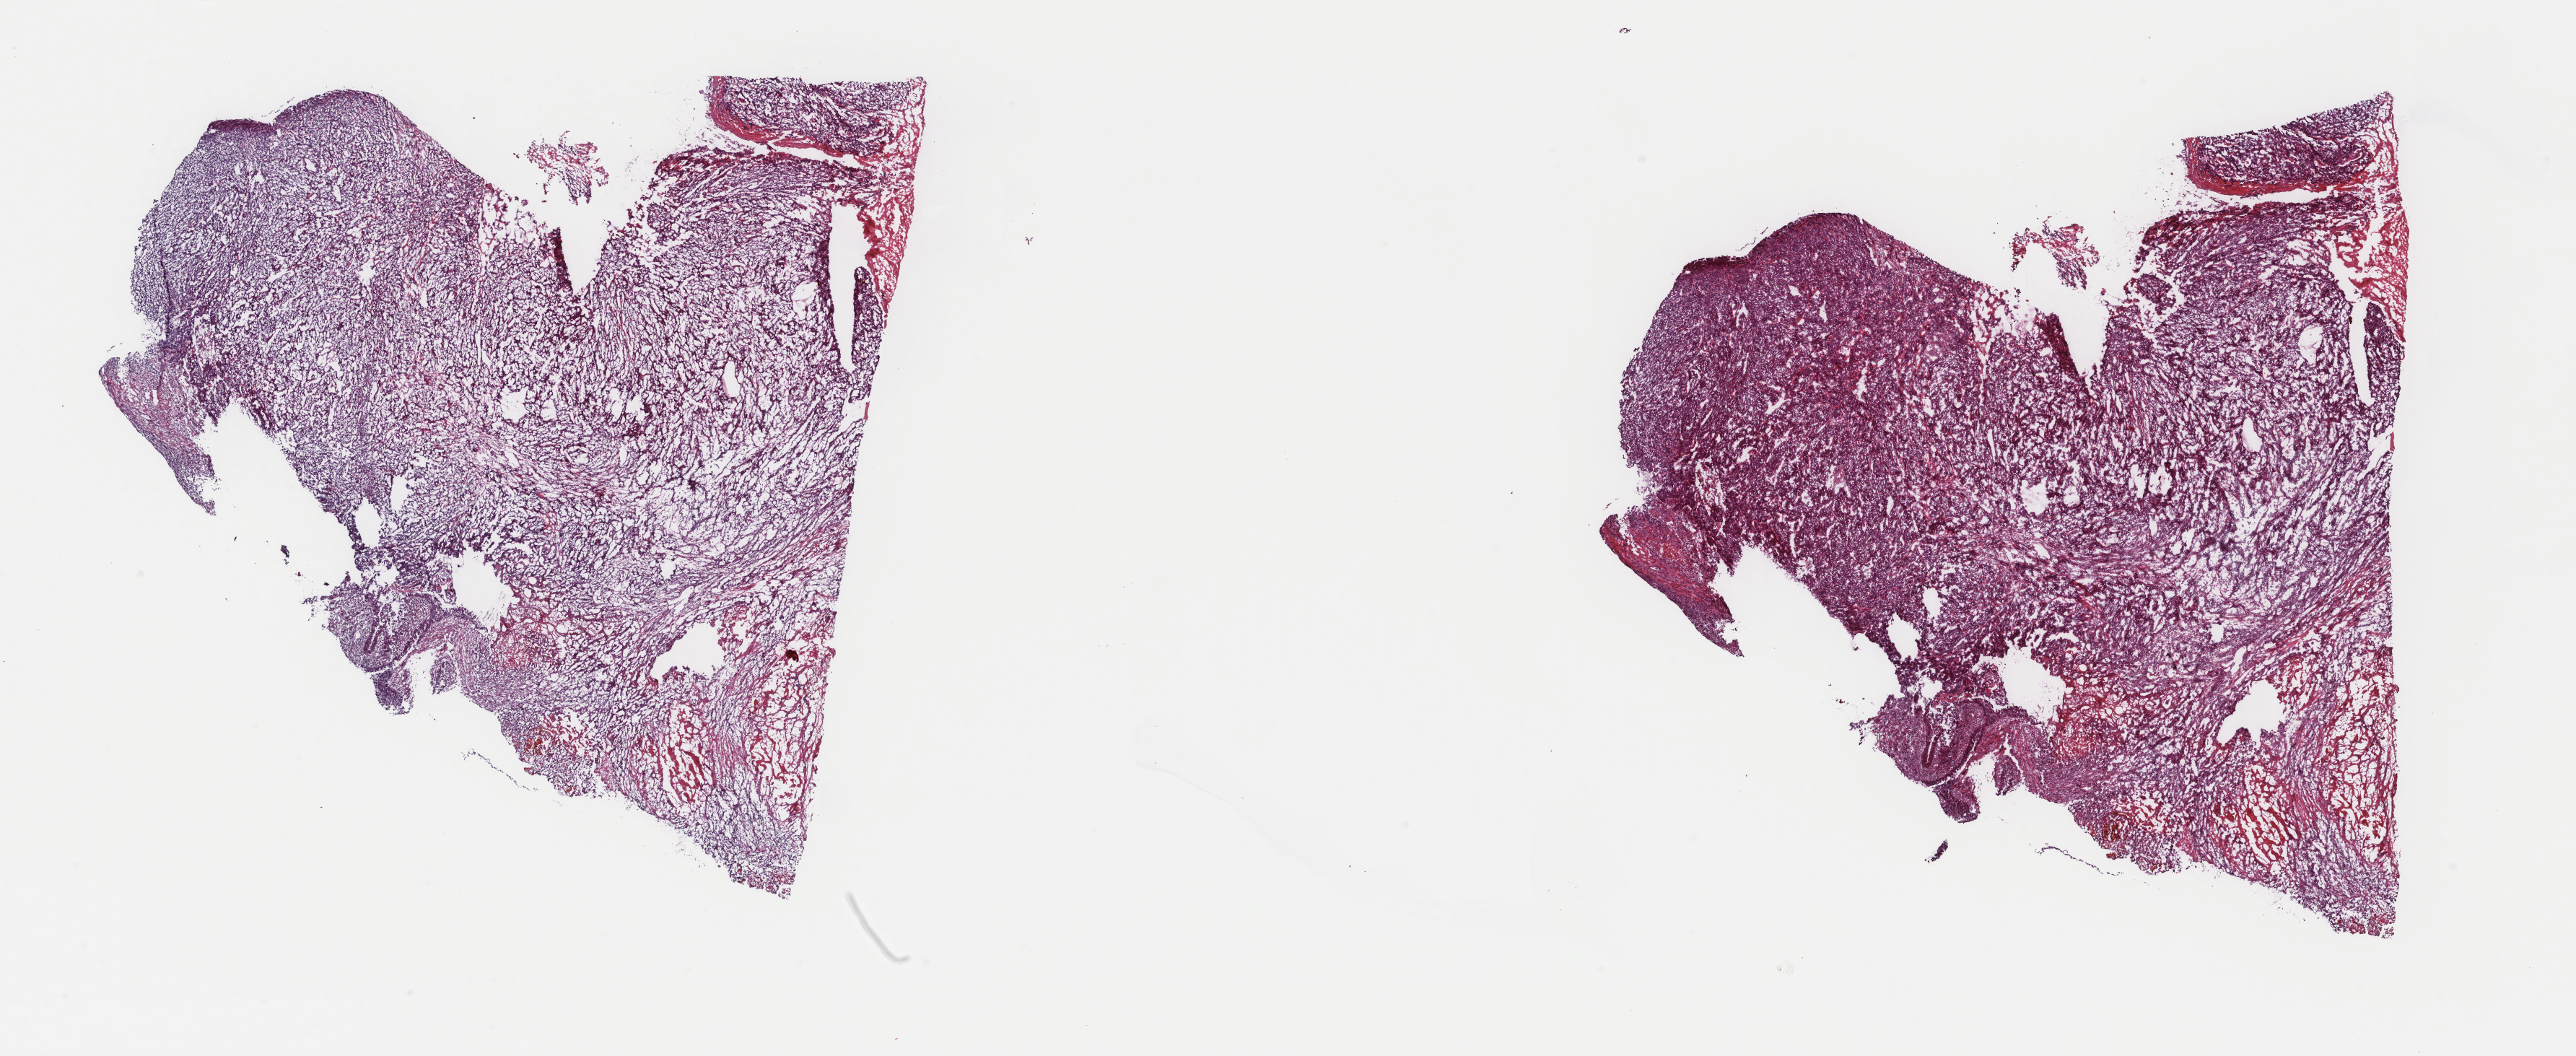
Whole-slide histology image, Hematoxylin and eosin (H&E) stained — shown as a low-resolution overview of the whole scanned area (about 28.3 x 11.6 mm, slide scanned at 40x); frozen section from the top of the tissue portion; sample: primary tumour, bladder. Male, age 76 years at initial diagnosis. Histologic grade: high grade. Slide review estimates, as recorded: tumour cells 85%, tumour nuclei 90%, normal cells 5%, stromal cells 8%, necrosis 2%. Inflammatory infiltration, as recorded: lymphocyte infiltration 0%, monocyte infiltration 0%, neutrophil infiltration 0%.
TNM: T3b N0 M0. Lymph nodes positive (case pathology): 0 of 28 examined. Pathologic diagnosis: Transitional cell carcinoma (lateral wall of bladder). AJCC pathologic stage: III (7th edition).